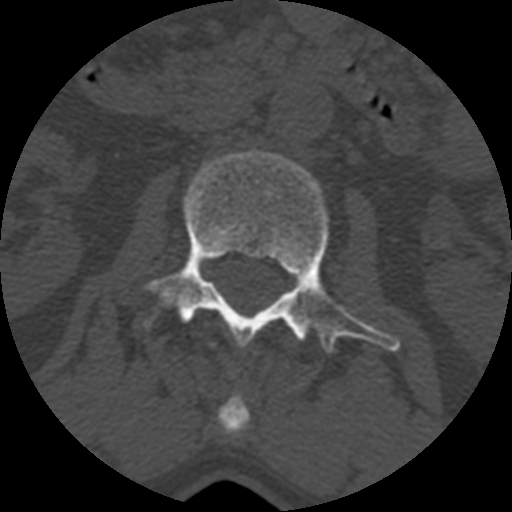
CT including the spine, one axial slice; slice 335 of 399 in the series (ordered by position); reconstruction kernel STANDARD; 120 kVp; bone window (W 1800 / L 400 HU); 1.25 mm slice thickness; 512 × 512 image matrix, field of view 160 × 160 mm. Patient age 71 years. Case-level facts recorded for this patient, not image findings: primary cancer: prostate.
Structures marked on this image (semi-automatically segmented with operator editing):
- L1 vertebra: bounding box [x1, y1, x2, y2] px = [218, 395, 248, 435]
- L2 vertebra: [106, 150, 402, 351]